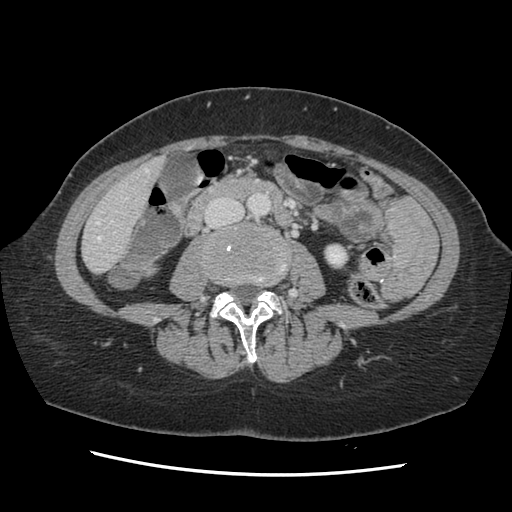
Contrast-enhanced abdominal CT, one axial slice; slice 34 of 141 in the series (ordered by position); soft-tissue window (W 400 / L 40 HU); 512 × 512 image matrix, field of view 330 × 330 mm. Female patient, age 61 years. From the clinical record (not read from this slice): diagnosis: colorectal cancer liver metastases, imaged before liver resection; multiple liver metastases: no; largest metastasis: 2.4 cm; disease in both lobes: no.
Outlined on this slice (manually delineated by an expert):
- hepatic veins: bounding box <97,169,149,240> (left, top, right, bottom; pixels)
- liver: <84,160,161,273>
- planned liver remnant (the part of the liver to remain after resection): <84,161,162,273>